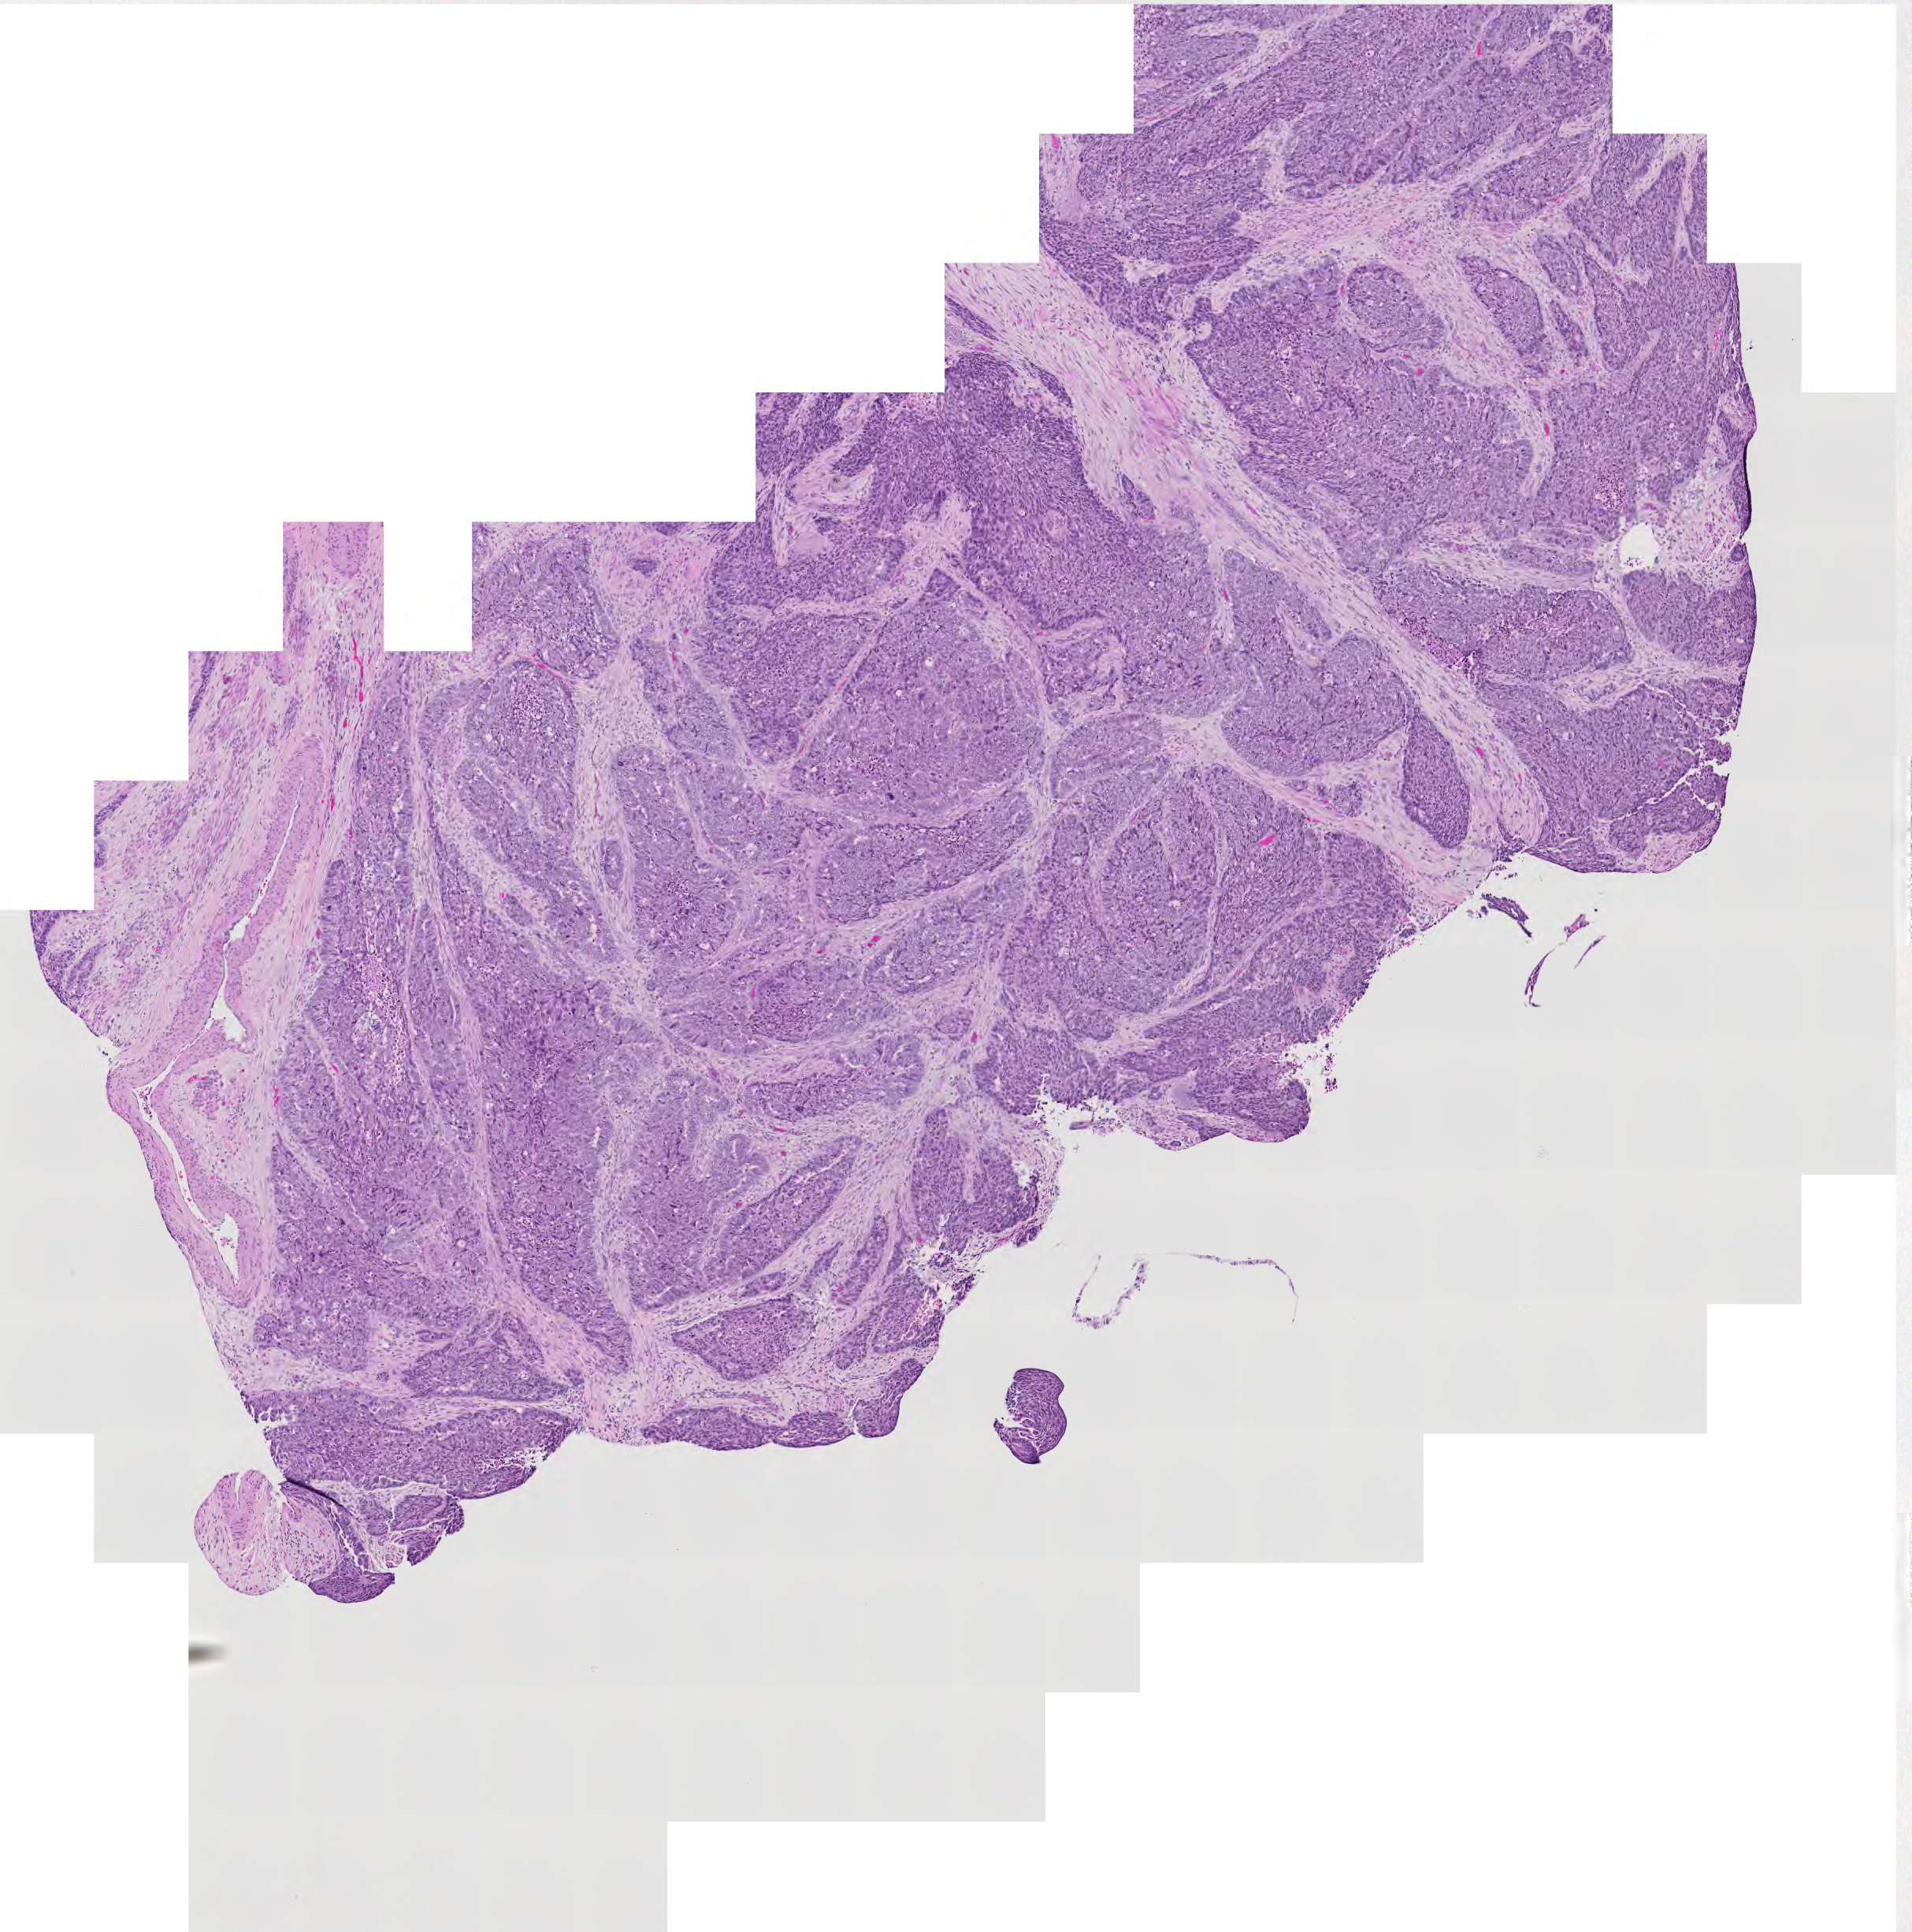
H&E whole-slide image, shown as a low-resolution overview of the whole scanned area (about 6.3 x 6.3 mm, slide scanned at 20x). Uterus, tumour tissue. Patient: female, age 65 years. Histologic grade: G3 (poorly differentiated).
AJCC pathologic stage: IV. Diagnosis: Endometrioid adenocarcinoma, NOS.